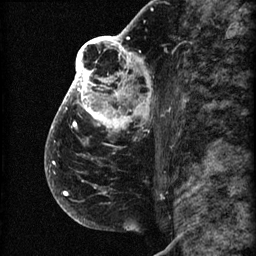
Breast MRI (dynamic contrast-enhanced), one sagittal slice. Slice 42 of 60 in the series (ordered by position). 3 images stored at this slice position (order not interpretable as contrast timing). 1.5 T. TE 4.2 ms, TR 22.7 ms. 2 mm slice thickness. 256 × 256 image matrix, field of view 180 × 180 mm. Female patient, age 48 years. From the clinical record (not read from this slice): setting: breast cancer imaged before/during neoadjuvant chemotherapy; receptor status: triple-negative.
Annotated regions visible in this slice (semi-automatic segmentation, software-assisted and operator-edited):
- analysis volume of interest (the breast-tissue region the enhancement analysis was run in; not a lesion): bounding box [x1, y1, x2, y2] px = [44, 30, 173, 207]
- tumour enhancement mask (voxels above the 90 % enhancement threshold inside the analysis volume of interest): [45, 30, 153, 196]